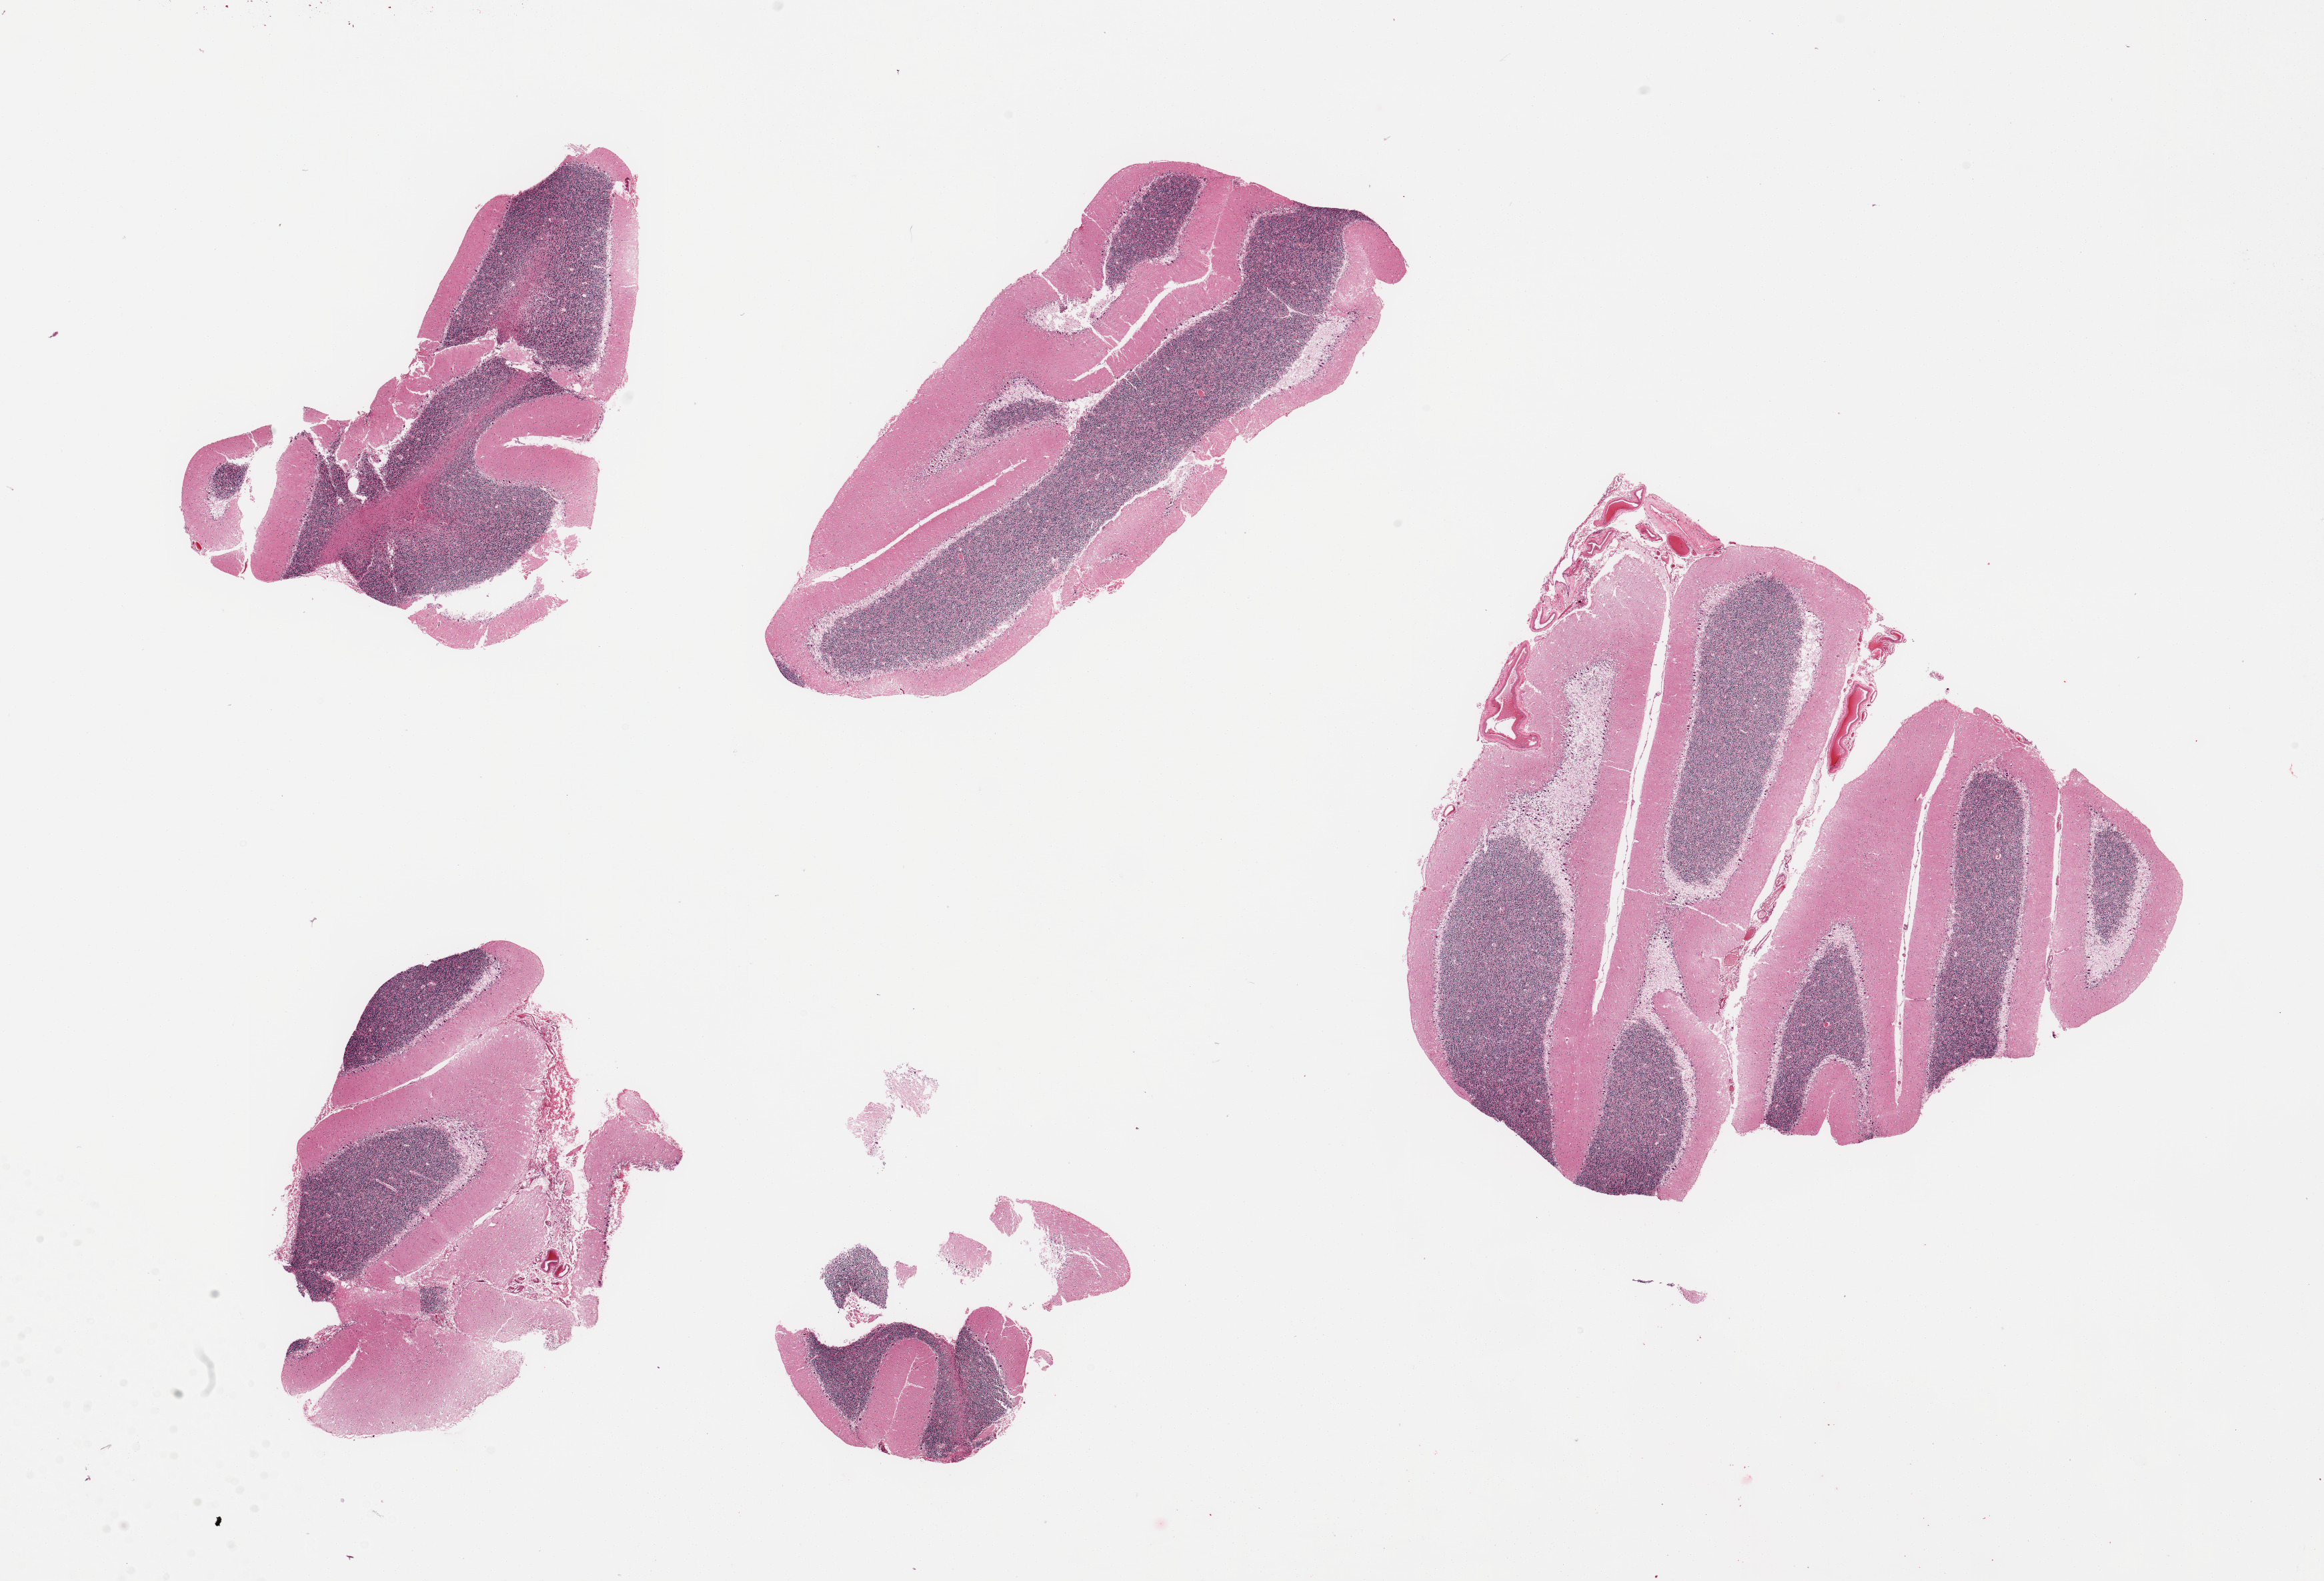
Whole-slide image, haematoxylin and eosin stain — low-resolution overview of the scanned area, about 27.6 x 18.8 mm. PAXgene-fixed, paraffin-embedded tissue. Target tissue: cerebellum. Donor tissue sample. Donor sex: male.
Review note (as recorded): 4 pieces, no abnormalities.